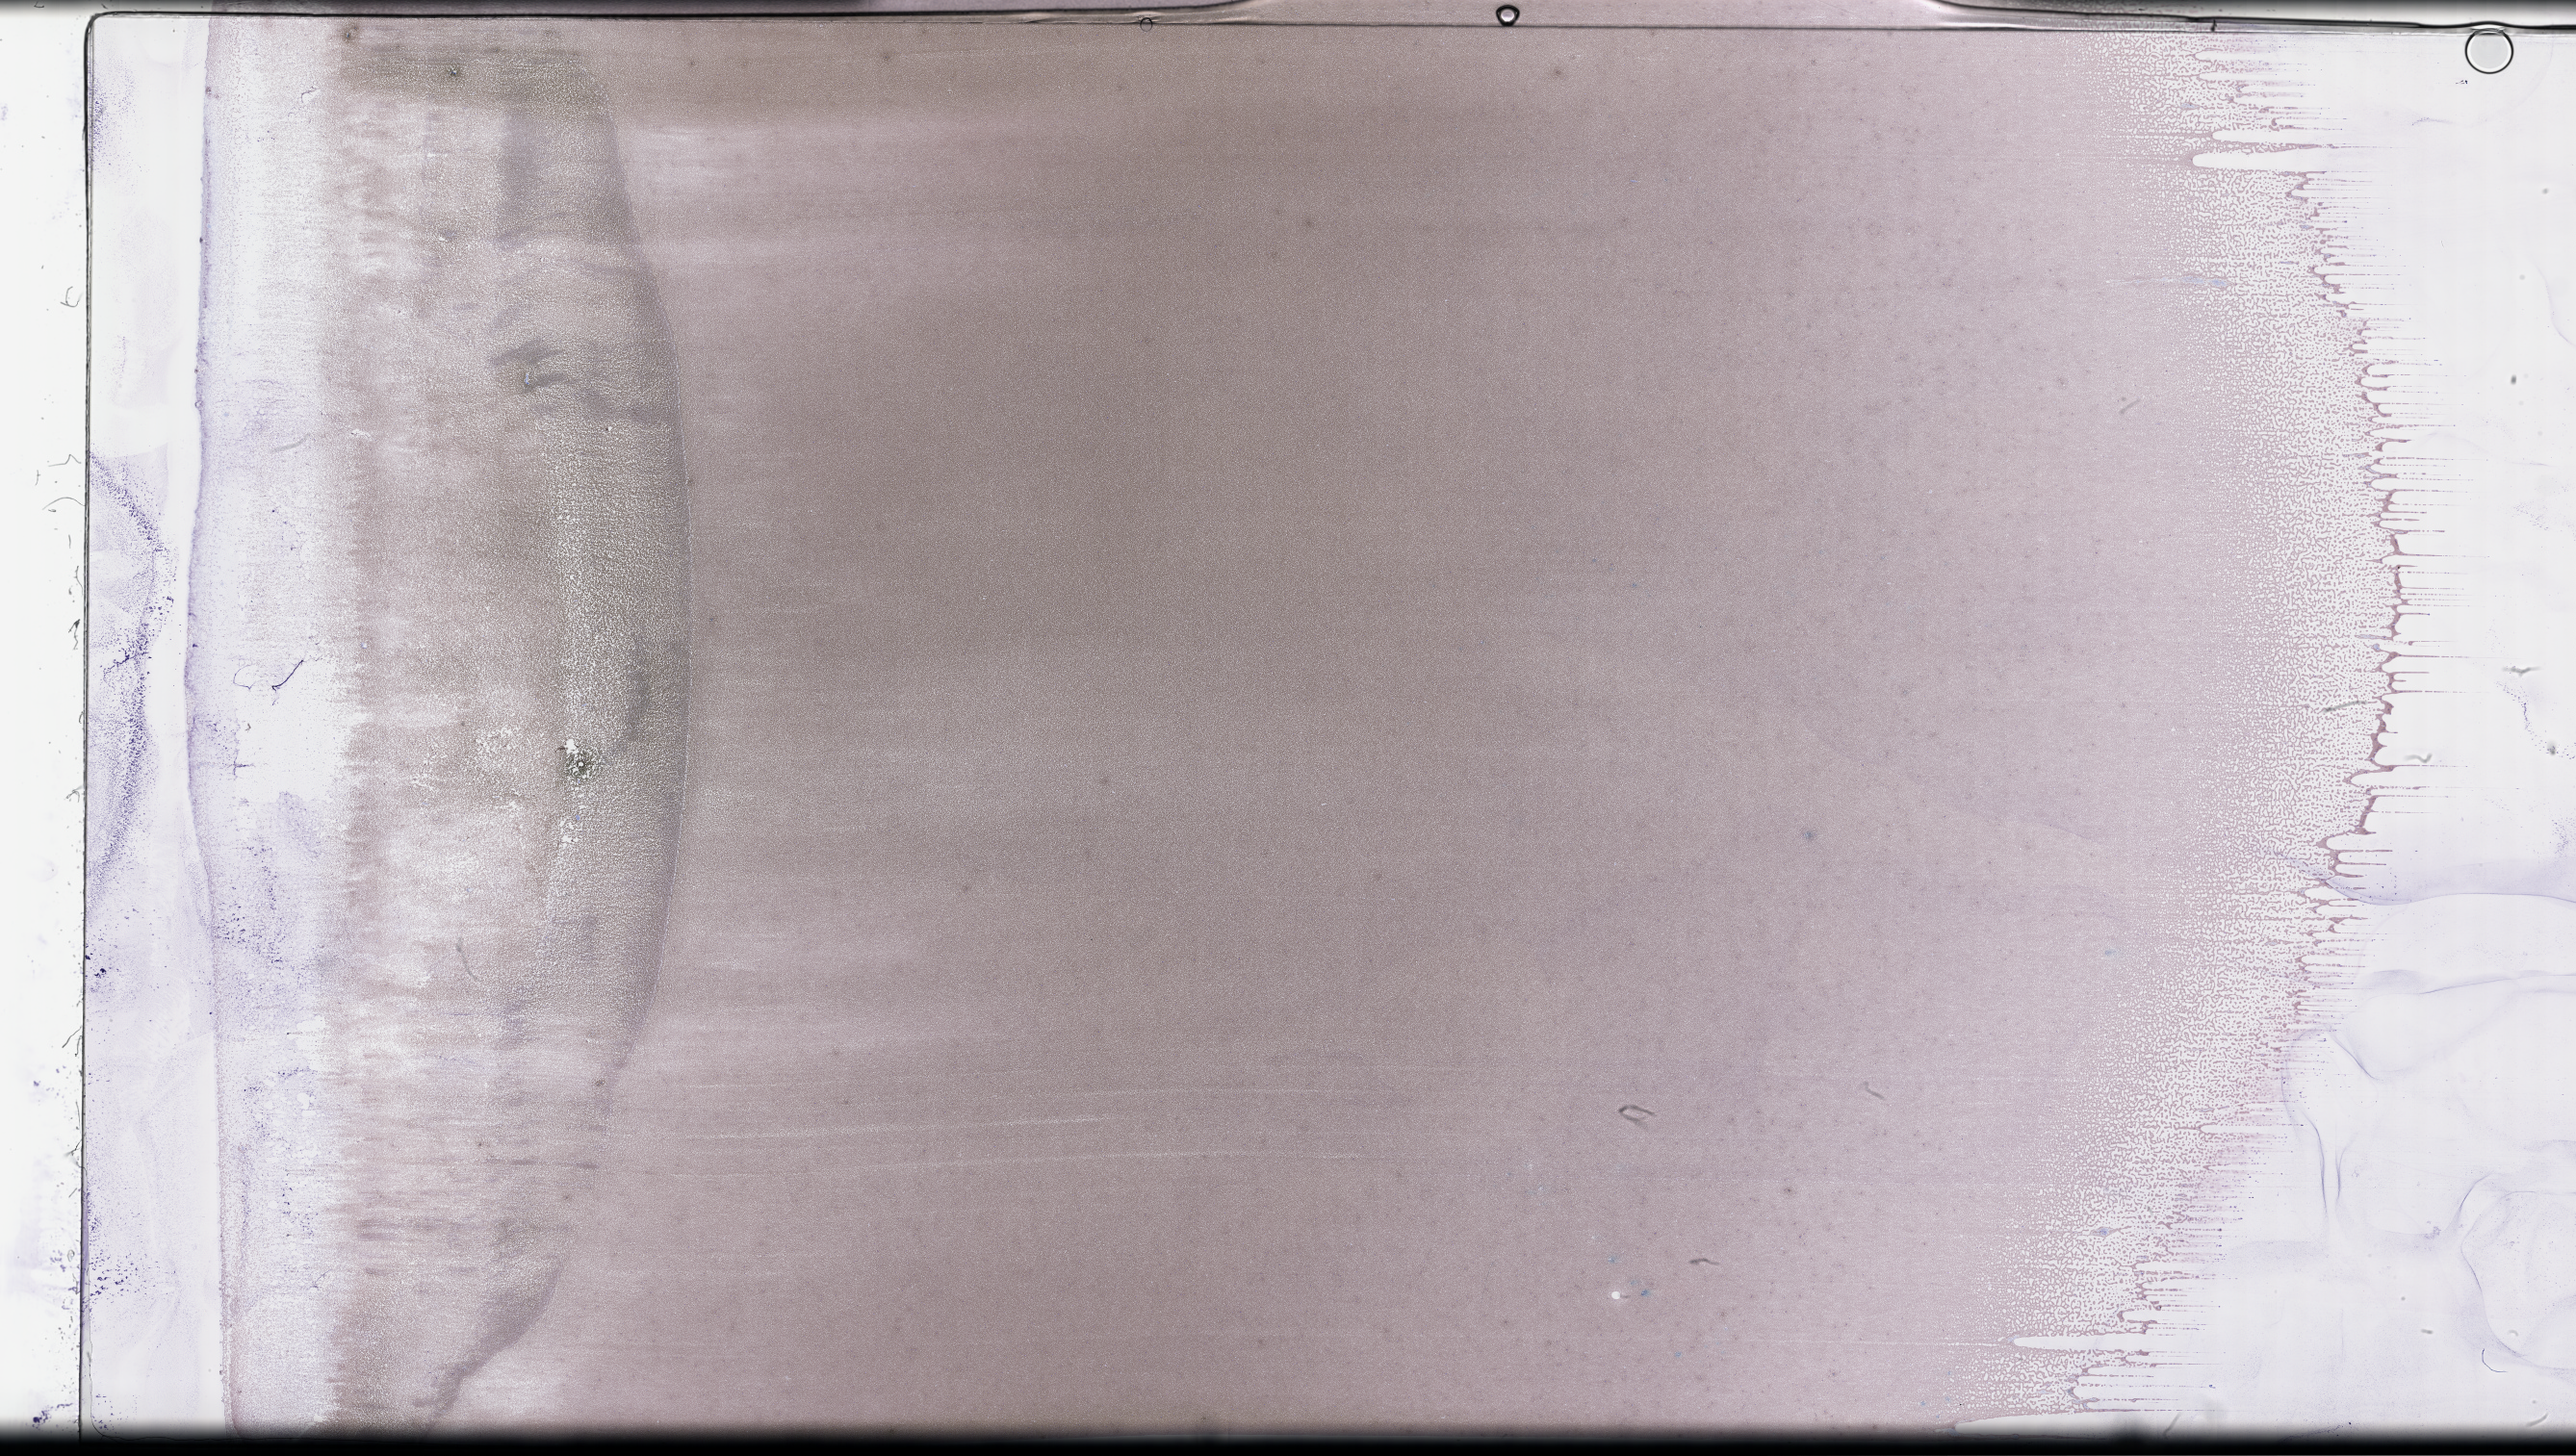
Whole-slide image of a whole blood smear, Wright-Giemsa stain — shown as a low-resolution overview of the whole scanned area (about 43.2 x 24.4 mm). Smear from an EDTA sample. Specimen time point: collected on treatment. Female patient.
From a patient with: Plasma Cell Myeloma.